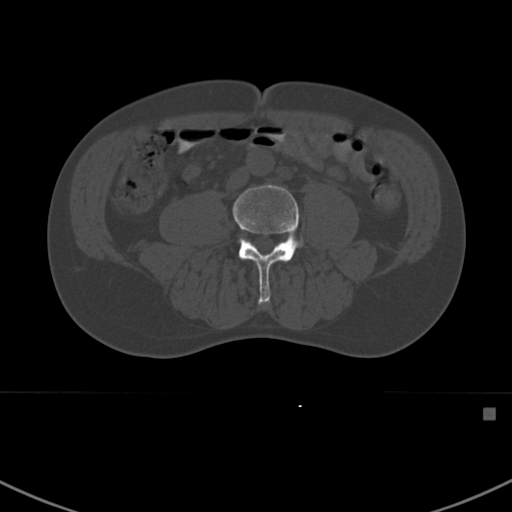
CT including the spine, one axial slice; reconstruction kernel Br40s; 120 kVp; bone window (W 1800 / L 400 HU); 512 × 512 image matrix. Patient: male, 59 years. Case-level facts recorded for this patient, not image findings: primary cancer: prostate.
Structures marked on this image (semi-automatic segmentation, software-assisted and operator-edited):
- L4 vertebra: box from (x=233, y=184) to (x=304, y=304) px